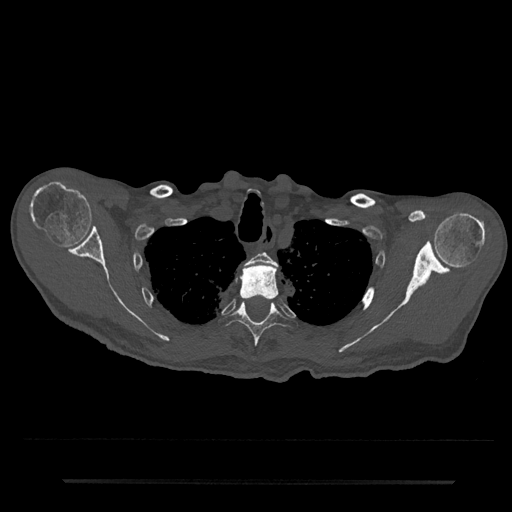
CT including the spine, one axial slice; slice 641 of 797 in the series (ordered by position); reconstruction kernel Br40s/3; bone window (W 1800 / L 400 HU); 0.5 mm slice thickness; 512 × 512 image matrix, field of view 427 × 427 mm. Male patient, age 74 years. From the clinical record (not read from this slice): primary cancer: prostate.
Annotated regions visible in this slice (semi-automatic segmentation, software-assisted and operator-edited):
- T2 vertebra: box from (x=244, y=252) to (x=277, y=268) px
- T3 vertebra: (x=240, y=259)–(x=279, y=300)
- T4 vertebra: (x=219, y=298)–(x=296, y=359)